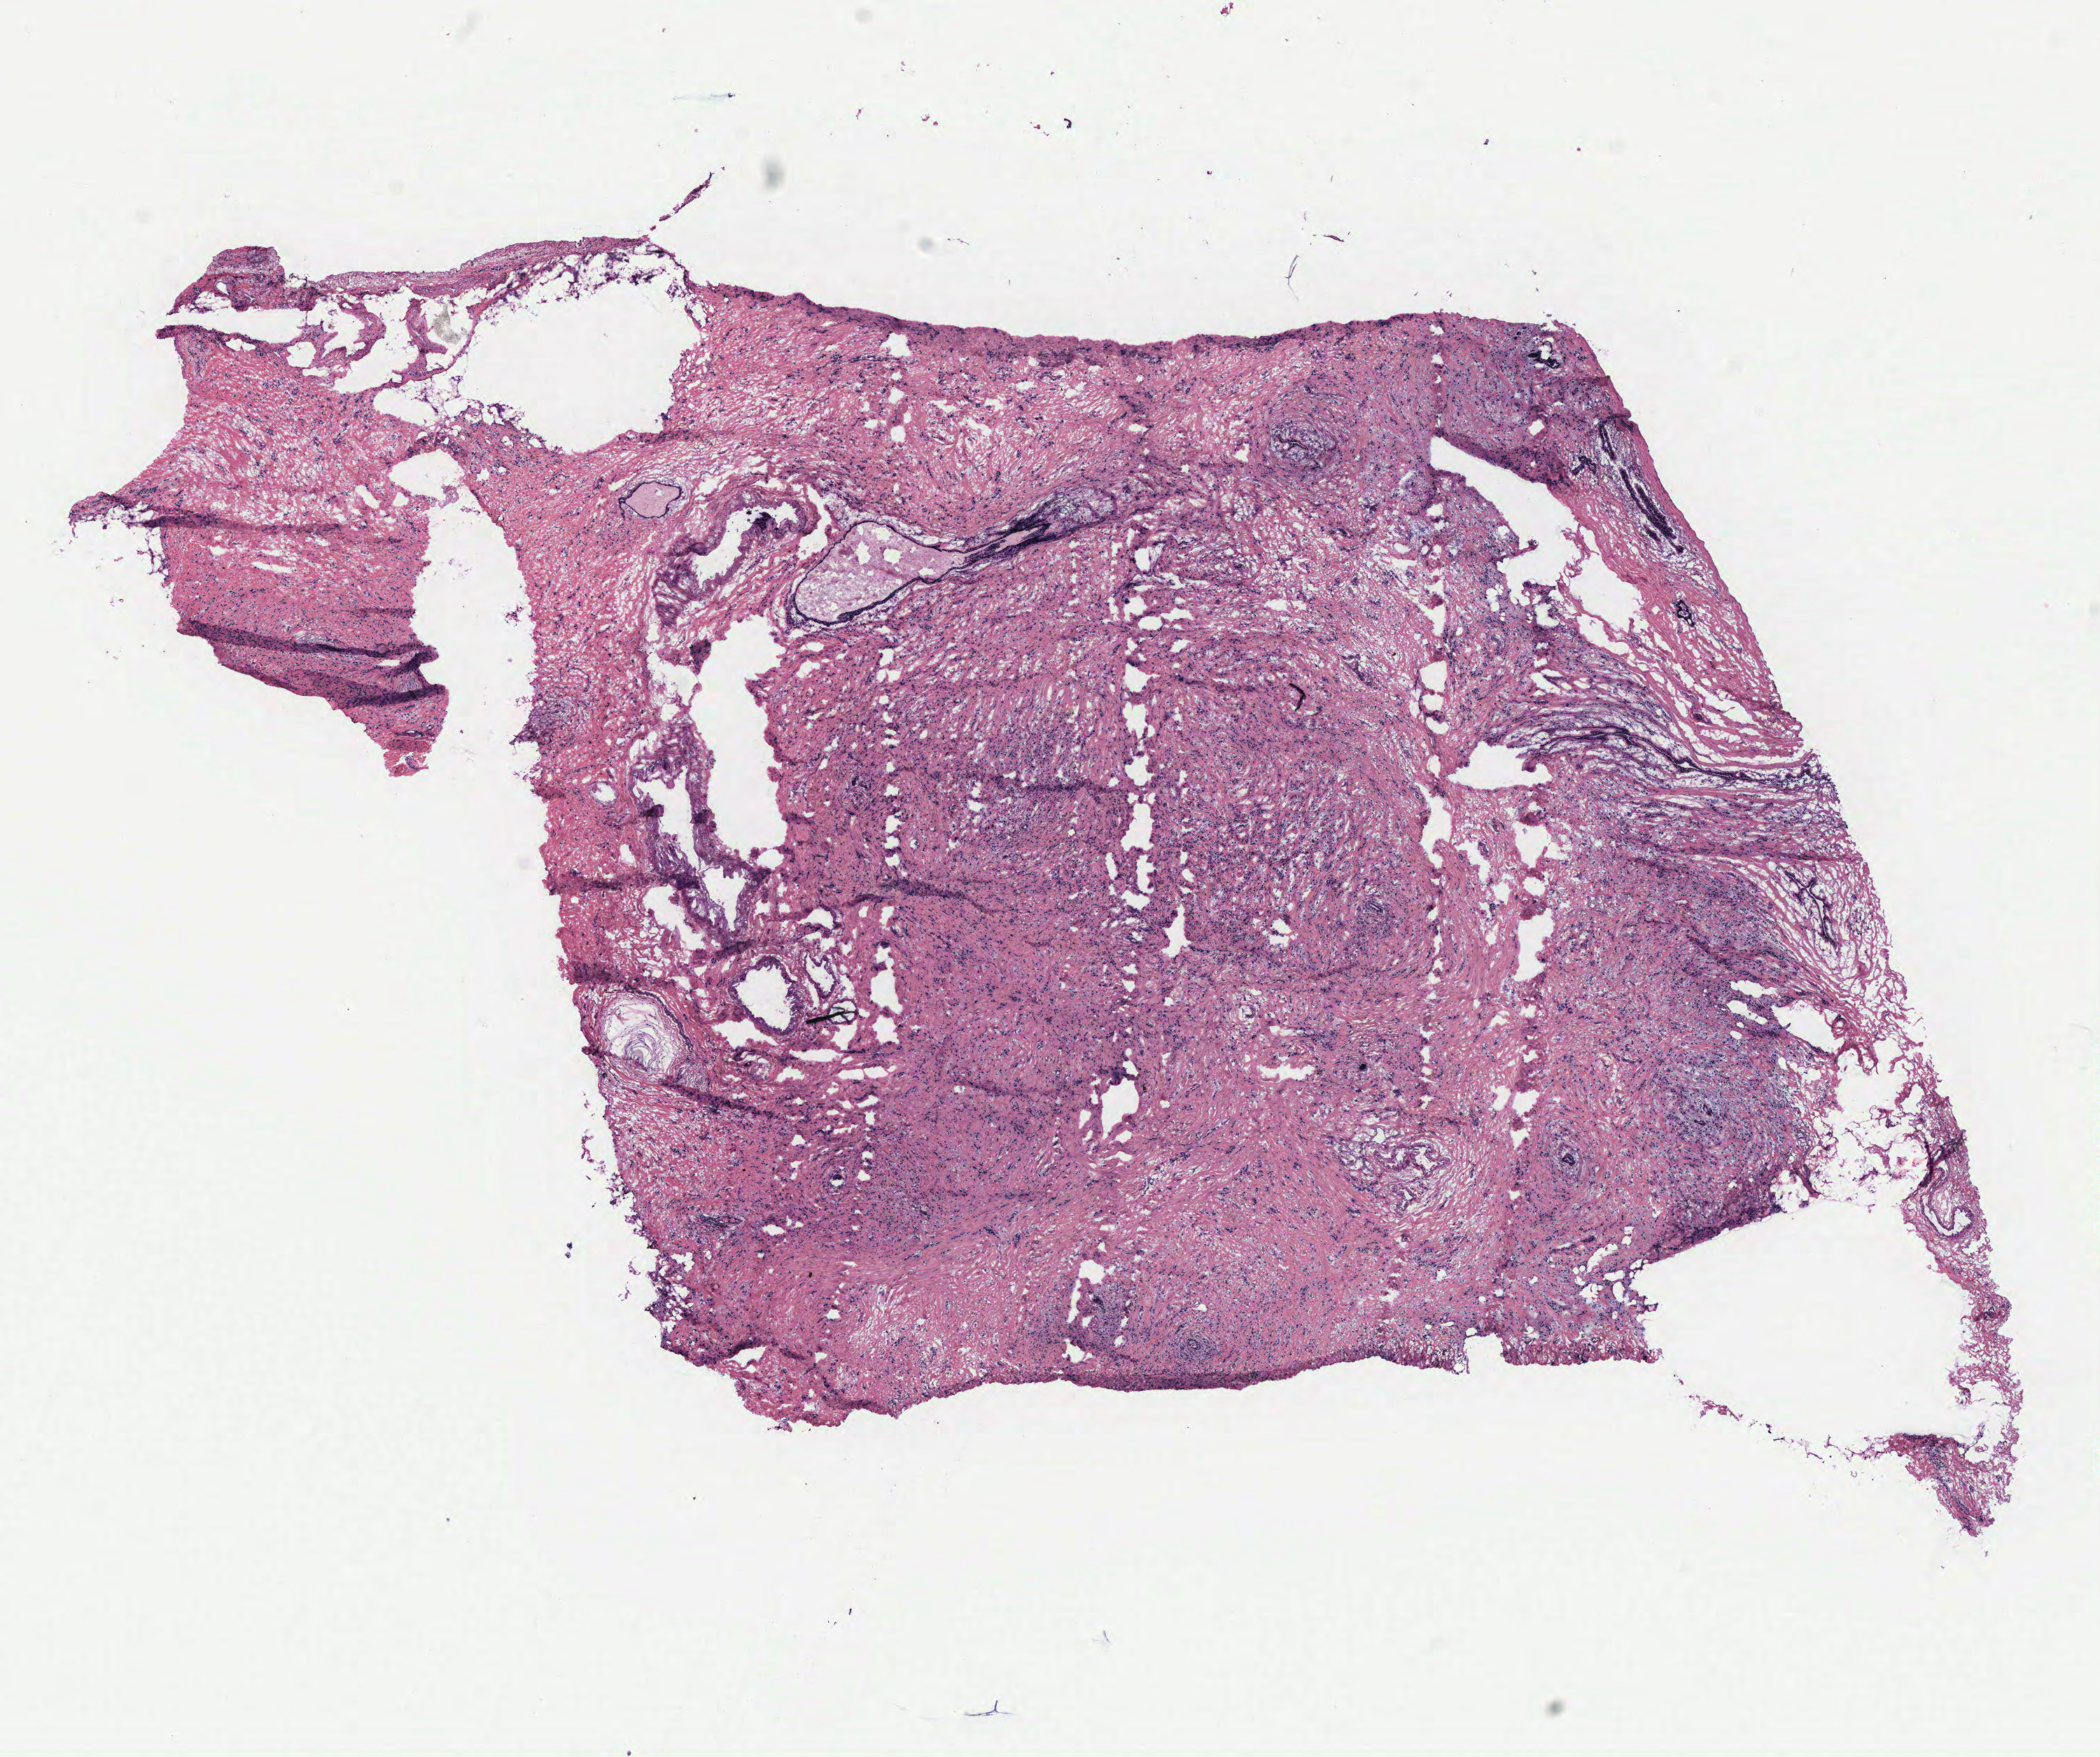
Digitized Hematoxylin and eosin (H&E) stained tissue section (whole slide), a low-resolution overview of the entire scanned area, about 12.0 x 10.0 mm (slide scanned at 40x); breast, tissue type not recorded. 63-year-old female patient.
Patient diagnosis: Infiltrating lobular carcinoma, NOS.